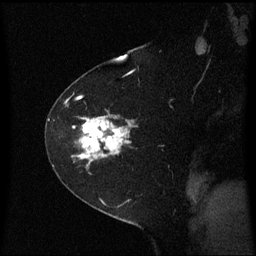
Breast MRI (dynamic contrast-enhanced), one sagittal slice; position 44 of 60 along the scan axis; dynamic contrast-enhanced series, image 2 of 3 at this slice position (ordered by acquisition); 1.5 T; TE 4.2 ms, TR 8.4 ms; 2 mm slice thickness; 256 × 256 image matrix, field of view 210 × 210 mm. Female patient, age 60 years. Case-level facts recorded for this patient, not image findings: setting: breast cancer imaged before/during neoadjuvant chemotherapy; receptor status: triple-negative.
Structures marked on this image (semi-automatically segmented with operator editing):
- analysis volume of interest (the breast-tissue region the enhancement analysis was run in; not a lesion): bounding box [x1, y1, x2, y2] px = [47, 99, 141, 180]
- tumour enhancement mask (voxels above the 70 % enhancement threshold inside the analysis volume of interest): [66, 100, 132, 165]